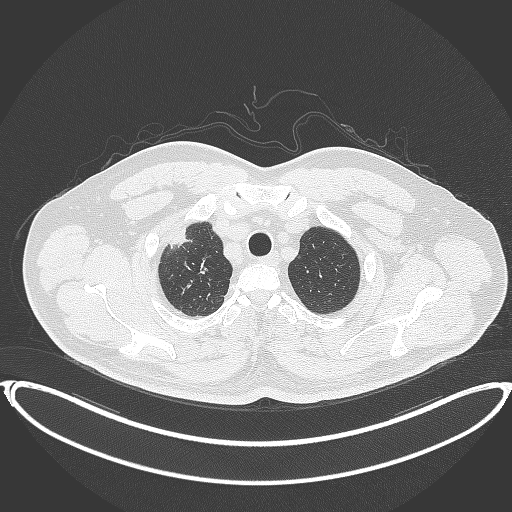
Chest CT, one axial slice; slice 344 of 399 in the series (ordered by position); lung window (W 1500 / L -600 HU); 1 mm slice thickness; 512 × 512 image matrix, field of view 445 × 445 mm. Male patient, age 53 years. Case-level facts recorded for this patient, not image findings: clinical TNM (as recorded): T2a N0 M0.
Structures marked on this image (rectangle marked by the reading radiologist):
- lung tumour (recorded histology: adenocarcinoma): box from (x=162, y=223) to (x=200, y=253) px